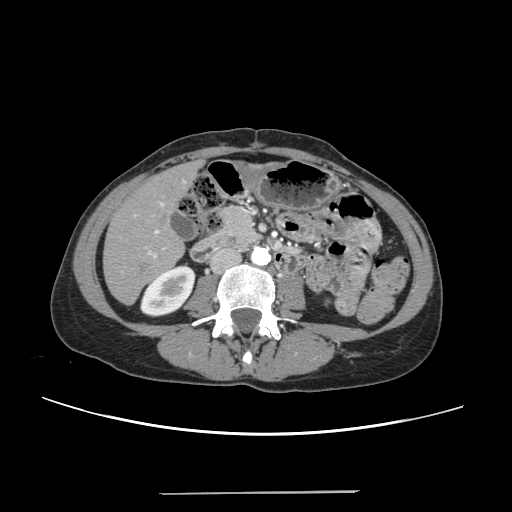
Contrast-enhanced abdominal CT, one axial slice. Slice 79 of 240 in the series (ordered by position). 120 kVp. Intravenous contrast given. Soft-tissue window (W 400 / L 40 HU). 1.25 mm slice thickness. 512 × 512 image matrix, field of view 371 × 371 mm. Female patient, age 60 years. From the clinical record (not read from this slice): diagnosis: colorectal cancer liver metastases, imaged before liver resection; multiple liver metastases: no; largest metastasis: 1.5 cm; chemotherapy before resection: yes.
Structures marked on this image (expert manual segmentation):
- liver: bounding box <105,164,197,304> (left, top, right, bottom; pixels)
- planned liver remnant (the part of the liver to remain after resection): <105,172,183,303>
- portal vein (with intrahepatic branches): <134,203,164,258>